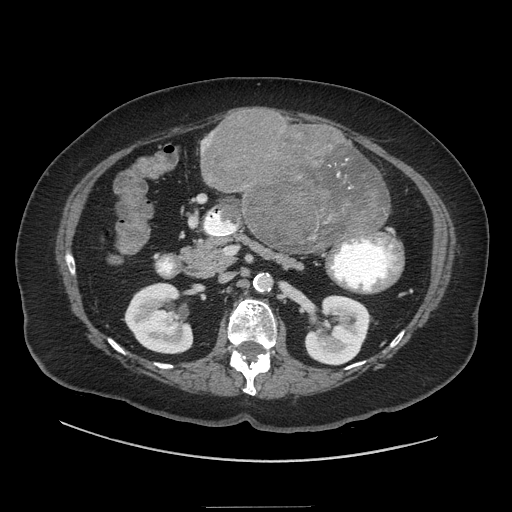
Contrast-enhanced abdominal CT (liver protocol), one axial slice; position 4 of 81 along the scan axis; 140 kVp; soft-tissue window (W 400 / L 40 HU); 2.5 mm slice thickness; 512 × 512 image matrix, field of view 440 × 440 mm. From the clinical record (not read from this slice): diagnosis: hepatocellular carcinoma (patient treated with transarterial chemoembolisation; whether this scan precedes or follows treatment is not stated here); TNM stage (as recorded): Stage-II; Child-Pugh class: A; tumour differentiation: moderately differentiated; tumour nodularity: multinodular.
Outlined on this slice (semi-automatically segmented with operator editing):
- liver parenchyma outside the tumour (the mass and vessels are separate outlines, so this box may not span the whole liver): bounding box [x1, y1, x2, y2] px = [206, 114, 390, 238]
- mass: [201, 111, 387, 251]